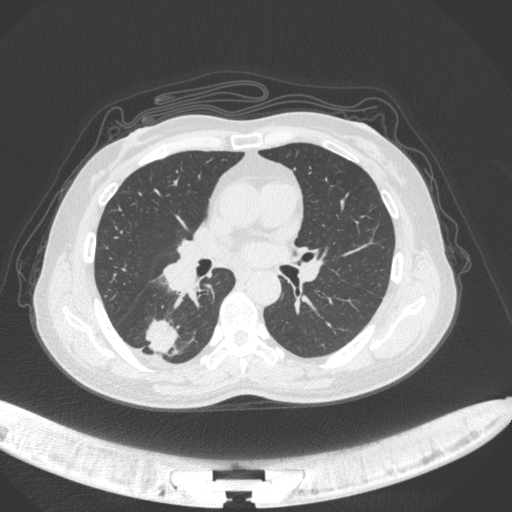
Chest CT, one axial slice; position 164 of 352 along the scan axis; lung window (W 1500 / L -600 HU); 1 mm slice thickness; 512 × 512 image matrix, field of view 400 × 400 mm. Patient: female, 55 years. Case-level facts recorded for this patient, not image findings: clinical TNM (as recorded): T1c N1 M0.
Structures marked on this image (rectangle marked by the reading radiologist):
- lung tumour (recorded histology: adenocarcinoma): box from (x=142, y=314) to (x=180, y=356) px